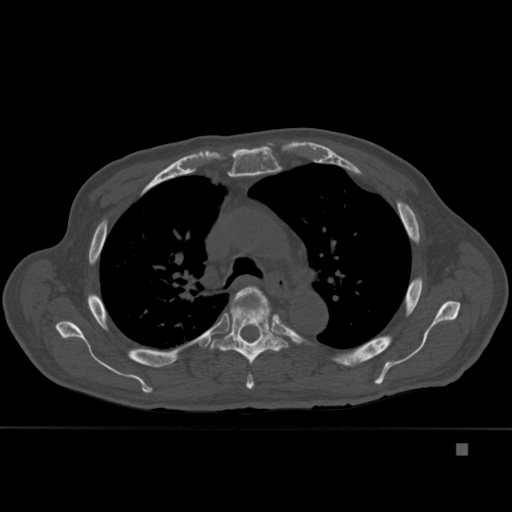
CT including the spine, one axial slice. Slice 310 of 451 in the series (ordered by position). Bone window (W 1800 / L 400 HU). 1.5 mm slice thickness. 512 × 512 image matrix. Patient: male, 75 years. Case-level facts recorded for this patient, not image findings: primary cancer: prostate.
Structures marked on this image (semi-automatic segmentation, software-assisted and operator-edited):
- T4 vertebra: bounding box [x1, y1, x2, y2] px = [225, 286, 276, 389]
- T5 vertebra: [210, 296, 289, 365]